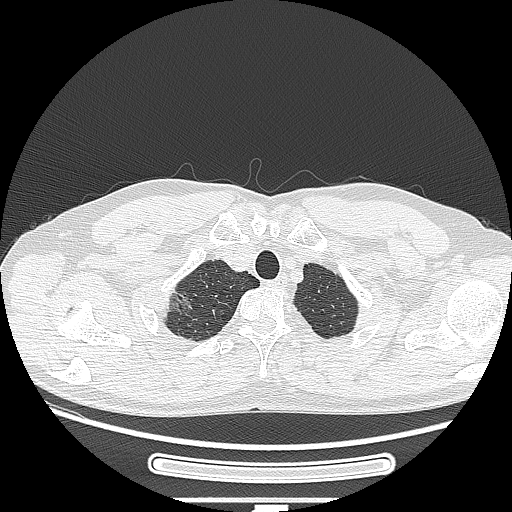
Chest CT, one axial slice. Position 239 of 269 along the scan axis. Reconstruction kernel LUNG. 120 kVp. Lung window (W 1500 / L -600 HU). 1.25 mm slice thickness. 512 × 512 image matrix, field of view 382 × 382 mm. Male patient, age 53 years. From the clinical record (not read from this slice): clinical TNM (as recorded): T1c N0 M0; histopathological grade: G2.
Structures marked on this image (bounding box drawn by a radiologist):
- lung tumour (recorded histology: adenocarcinoma): bounding box <158,285,191,315> (left, top, right, bottom; pixels)